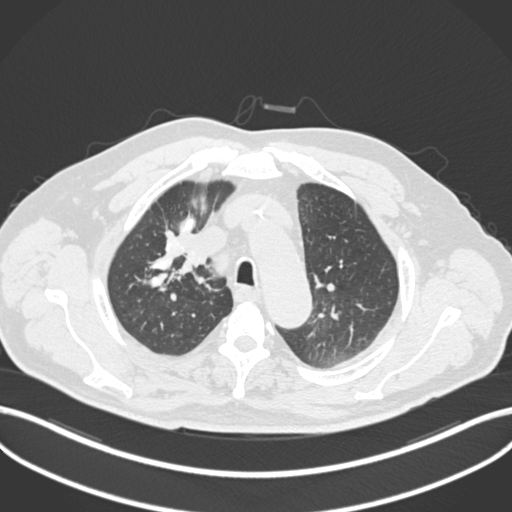
Chest CT, one axial slice. Reconstruction kernel B30f. Lung window (W 1500 / L -600 HU). 512 × 512 image matrix. Male patient, age 60 years. From the clinical record (not read from this slice): clinical TNM (as recorded): T1b N1 M0.
Outlined on this slice (bounding box drawn by a radiologist):
- lung tumour (recorded histology: squamous cell carcinoma): bounding box (x1, y1, x2, y2) in pixels: (164, 237, 206, 268)